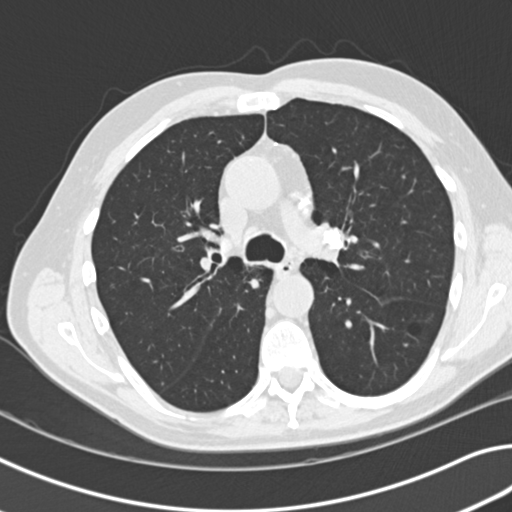
Chest CT (low-dose screening protocol), one axial image, baseline annual screen, lung window (W 1500 / L -600 HU), 2 mm slice thickness, slice 58 of 154 in the series. Male participant, aged 67 years at enrolment. Current smoker at enrolment.
Lesion marked by an expert reader, bounding box (x1, y1, x2, y2) in pixels: (229, 260, 282, 305). No non-calcified nodule or mass ≥4 mm was recorded by the screening reader at this exam. Official screen result: negative screen, significant abnormalities not suspicious for lung cancer. Participant outcome: lung cancer diagnosed 194 days after this screen — small cell carcinoma, NOS, right upper lobe, poorly differentiated (G3), stage IIIB (AJCC 6th edition), 50 mm at pathology.